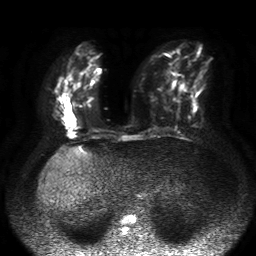
Breast MRI, one axial slice. Position 20 of 50 along the scan axis. Diffusion-weighted series; image 2 of 4 stored at this slice position (different b-values; order by instance number). 1.5 T. 4 mm slice thickness. 256 × 256 image matrix. Female patient.
Annotated regions visible in this slice (manually delineated by an expert):
- tumour on diffusion-weighted imaging: bounding box [x1, y1, x2, y2] px = [63, 113, 77, 128]